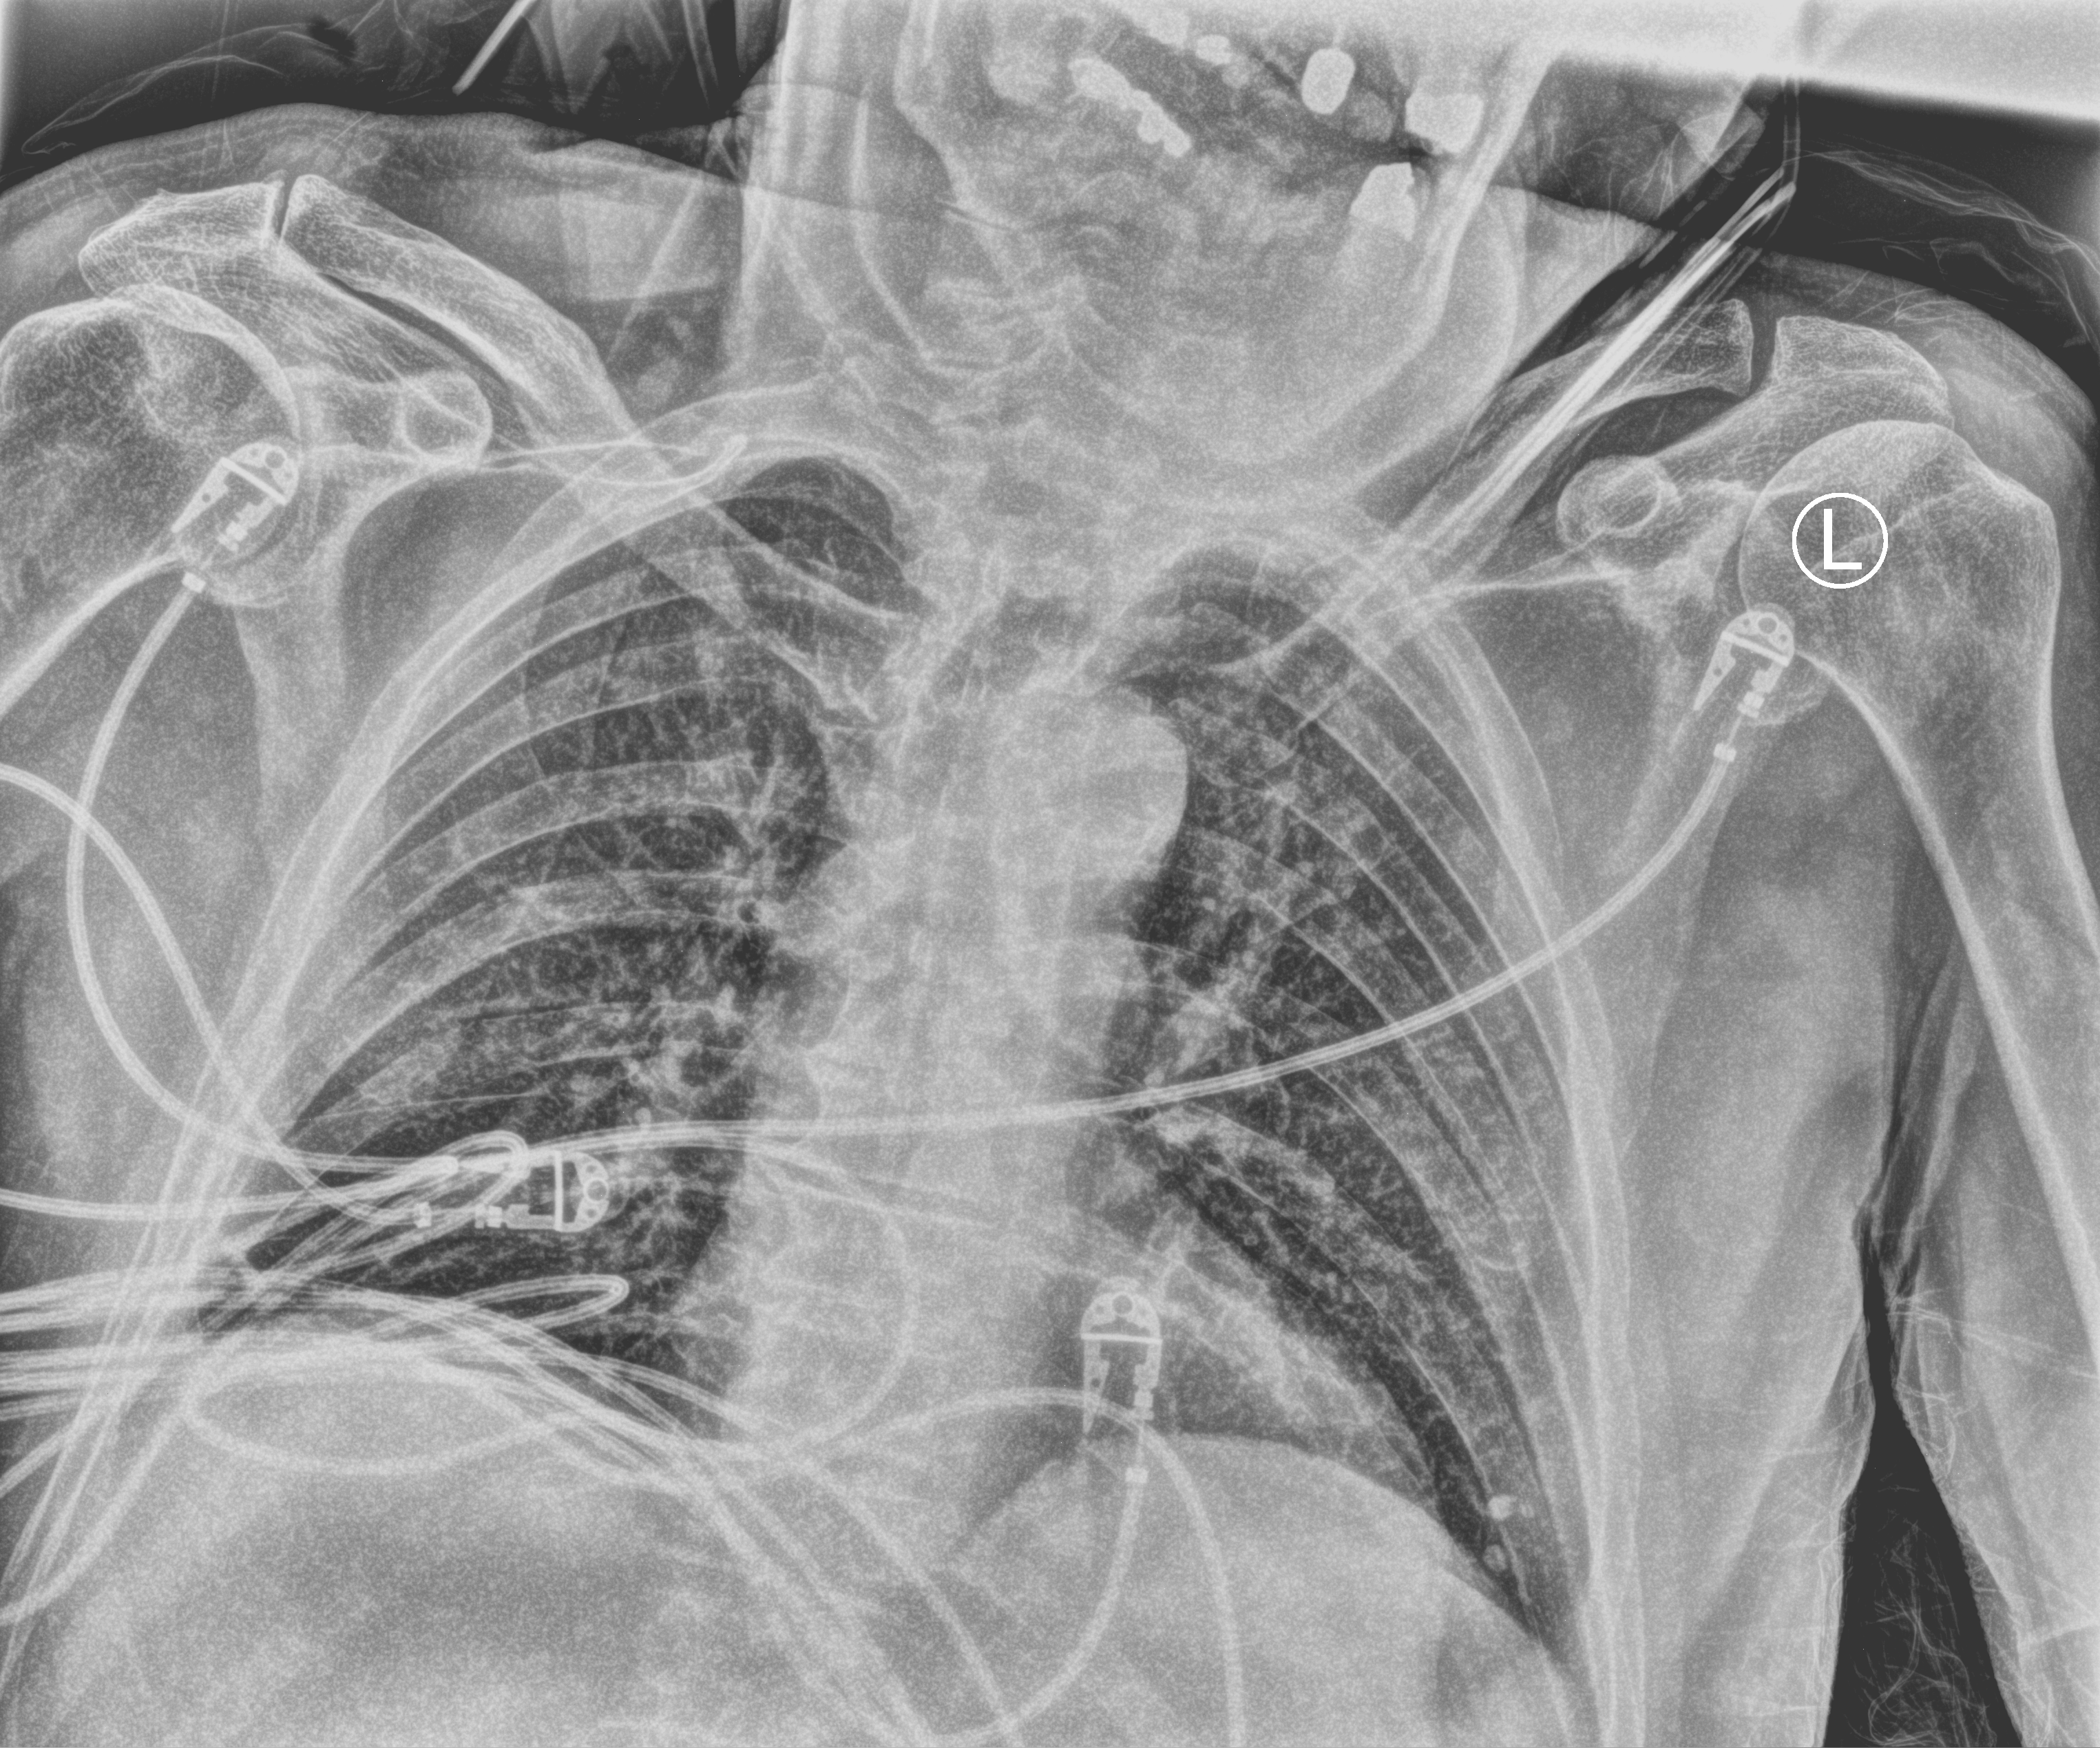
Portable chest radiograph; anteroposterior (AP) projection. Male patient hospitalised with COVID-19, age 75–90 years.
Hospital-stay facts (about this admission, not read from this image; timing relative to this image not recorded): admitted to intensive care during this hospital stay: no.